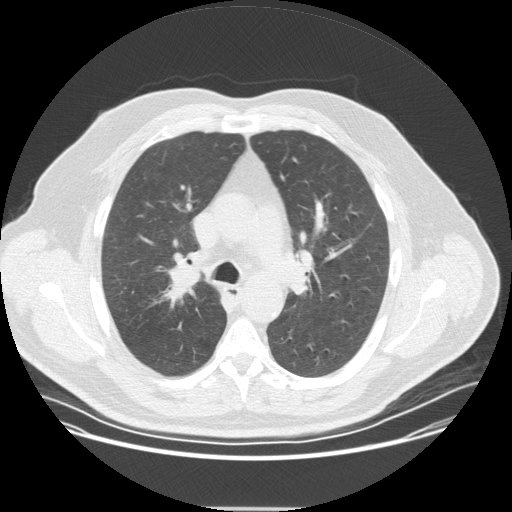
Chest CT (low-dose screening protocol), one axial image. Second annual screen. Lung window (W 1500 / L -600 HU). 512 × 512 image matrix, field of view 419 × 419 mm. Male, age 57 years at enrolment. Current smoker at enrolment.
Expert reader's lesion annotation, bounding box [x1, y1, x2, y2] px = [149, 251, 211, 310]. Reader record for this screening exam (exam-level; its link to the box is not recorded): non-calcified nodule or mass ≥4 mm, right upper lobe, 20 × 16 mm, spiculated (stellate) margins, soft tissue attenuation, pre-existing on the prior screen: no. Official screen result: positive, other.